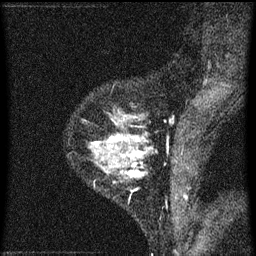
Breast MRI (dynamic contrast-enhanced), one sagittal slice; position 18 of 60 along the scan axis; dynamic contrast-enhanced series, image 2 of 3 at this slice position (ordered by acquisition); 1.5 T; TE 4.2 ms, TR 8 ms; 2 mm slice thickness; 256 × 256 image matrix. Female patient, age 33 years.
Annotated regions visible in this slice (semi-automatic segmentation, software-assisted and operator-edited):
- analysis volume of interest (the breast-tissue region the enhancement analysis was run in; not a lesion): bounding box (x1, y1, x2, y2) in pixels: (81, 118, 149, 185)
- tumour enhancement mask (voxels above the 70 % enhancement threshold inside the analysis volume of interest): (90, 136, 145, 177)